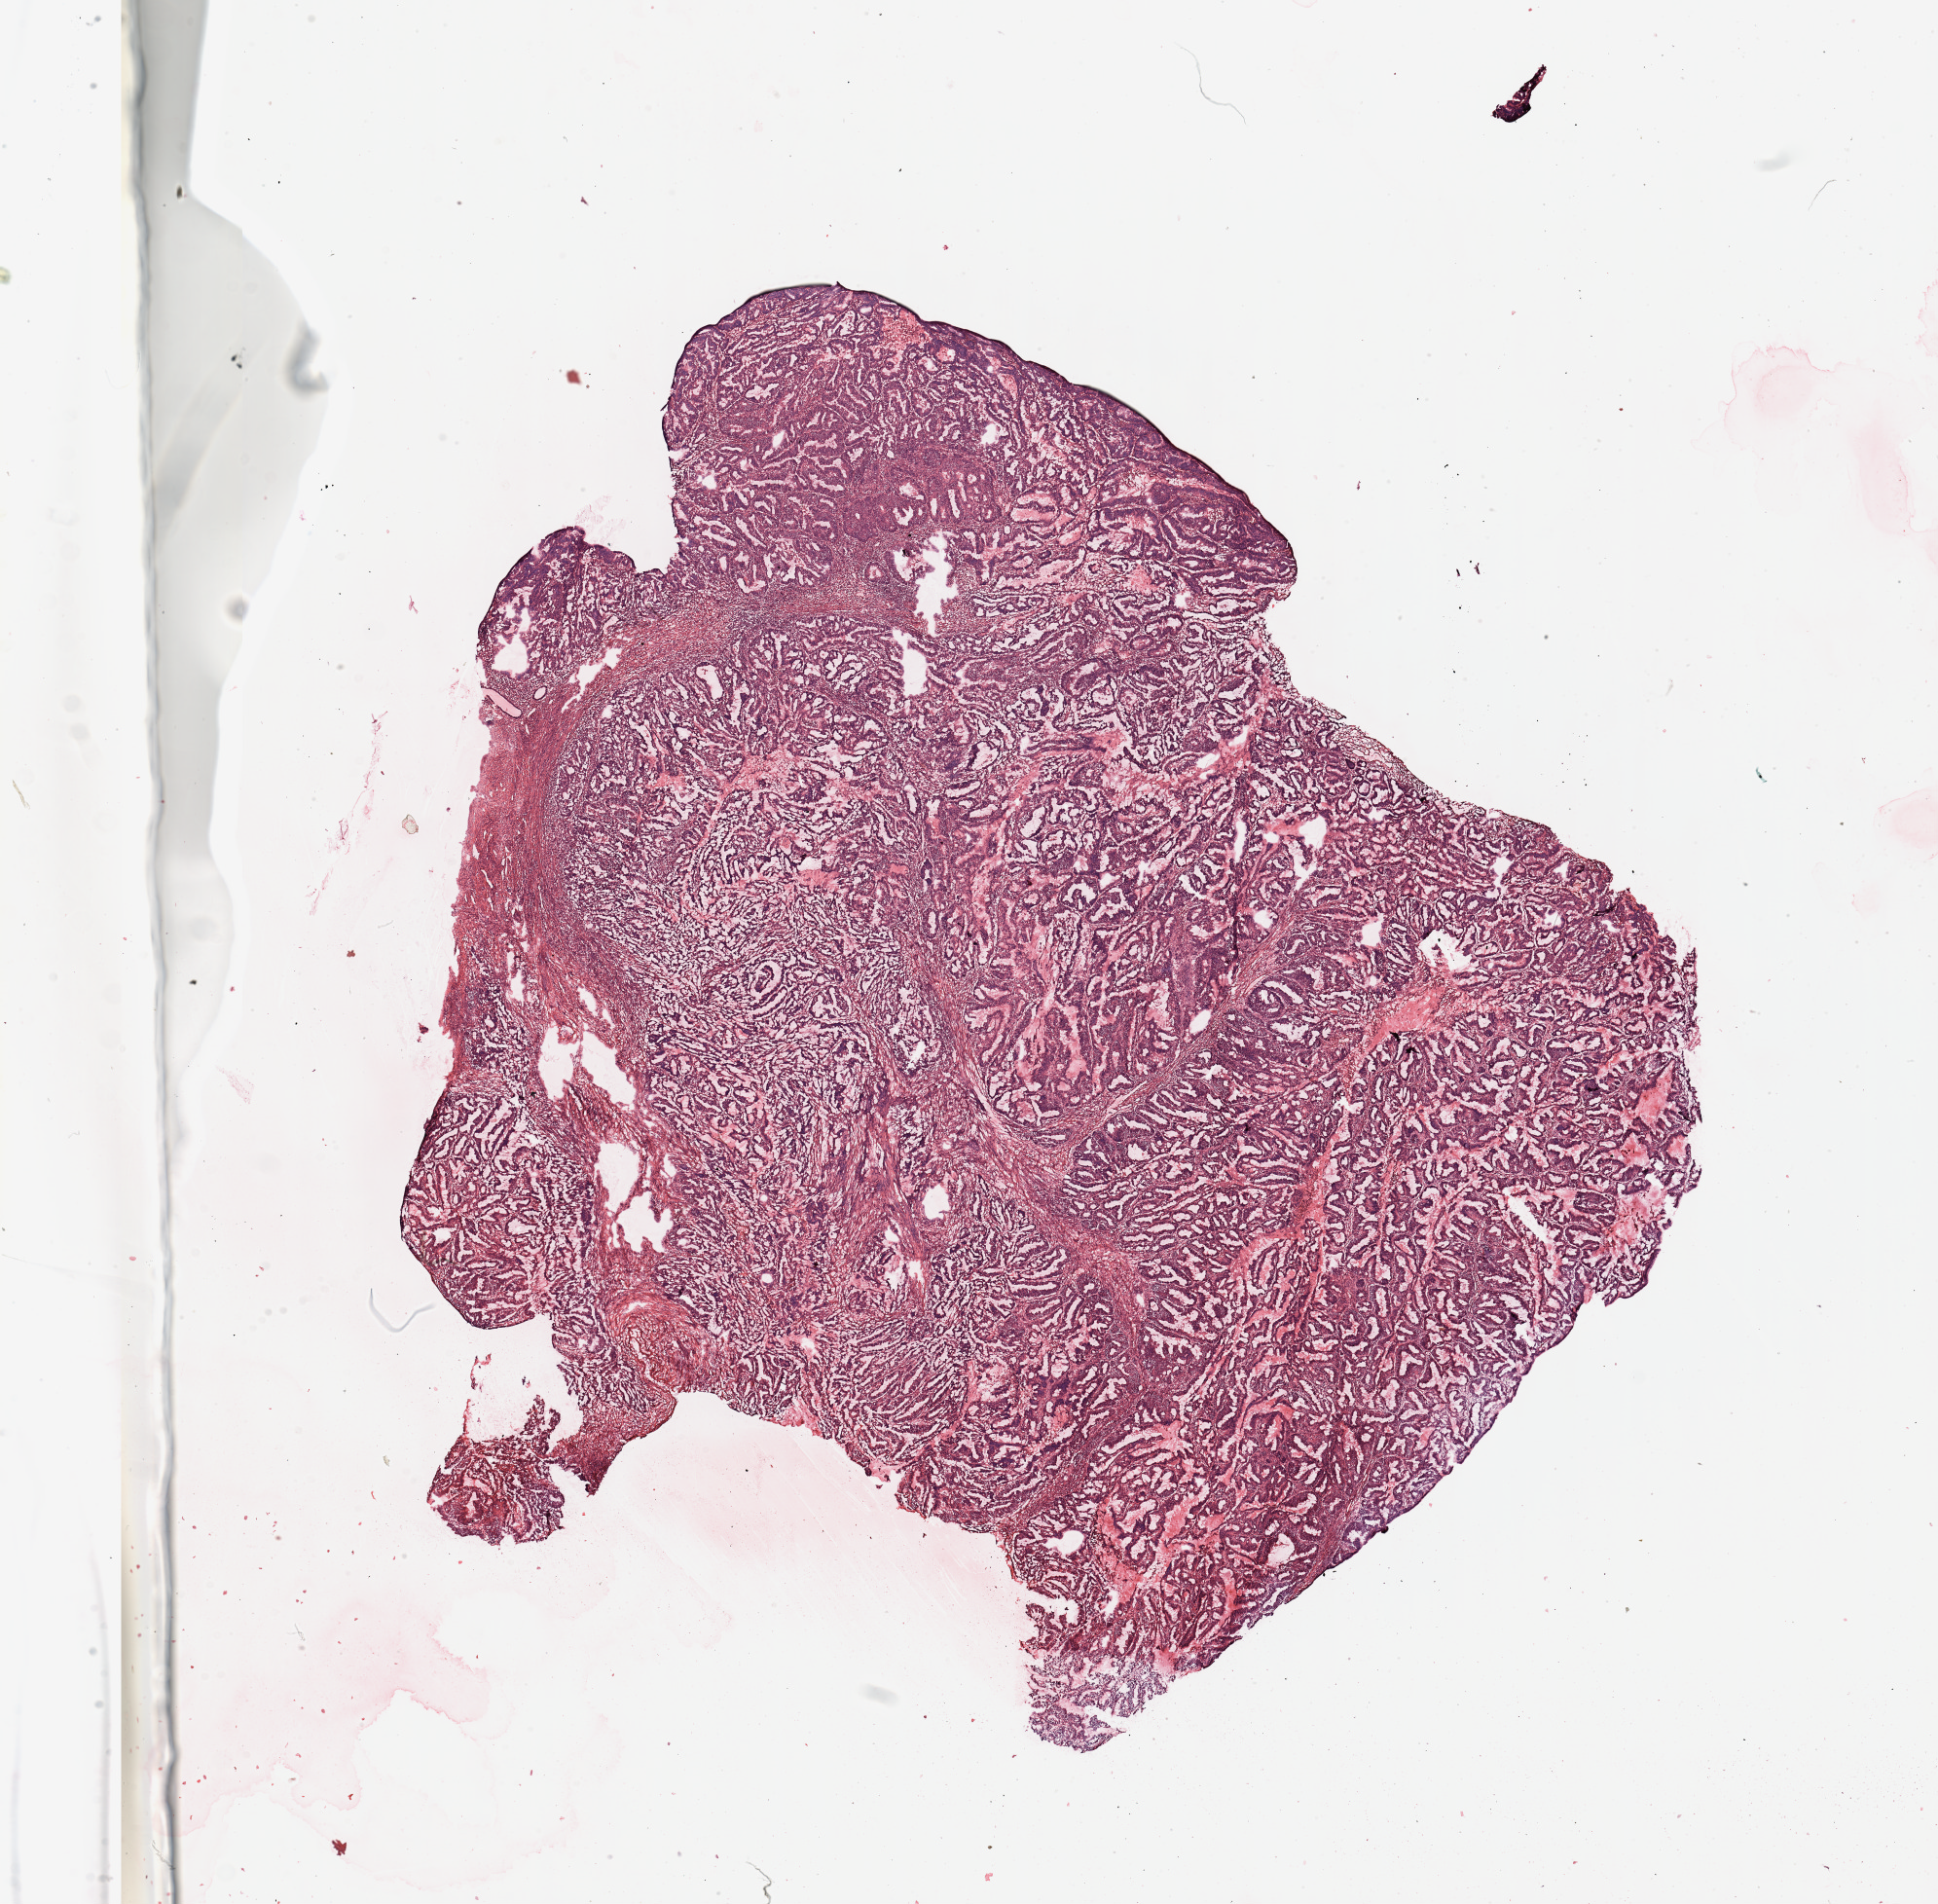
H&E whole-slide image — shown as a low-resolution overview of the whole scanned area (about 15.8 x 15.5 mm, acquisition: 20x scan). Tumour tissue sample, uterus. 65-year-old female patient. Histologic grade: G2 (moderately differentiated).
Diagnosis: Endometrioid adenocarcinoma, NOS. AJCC pathologic stage: I.